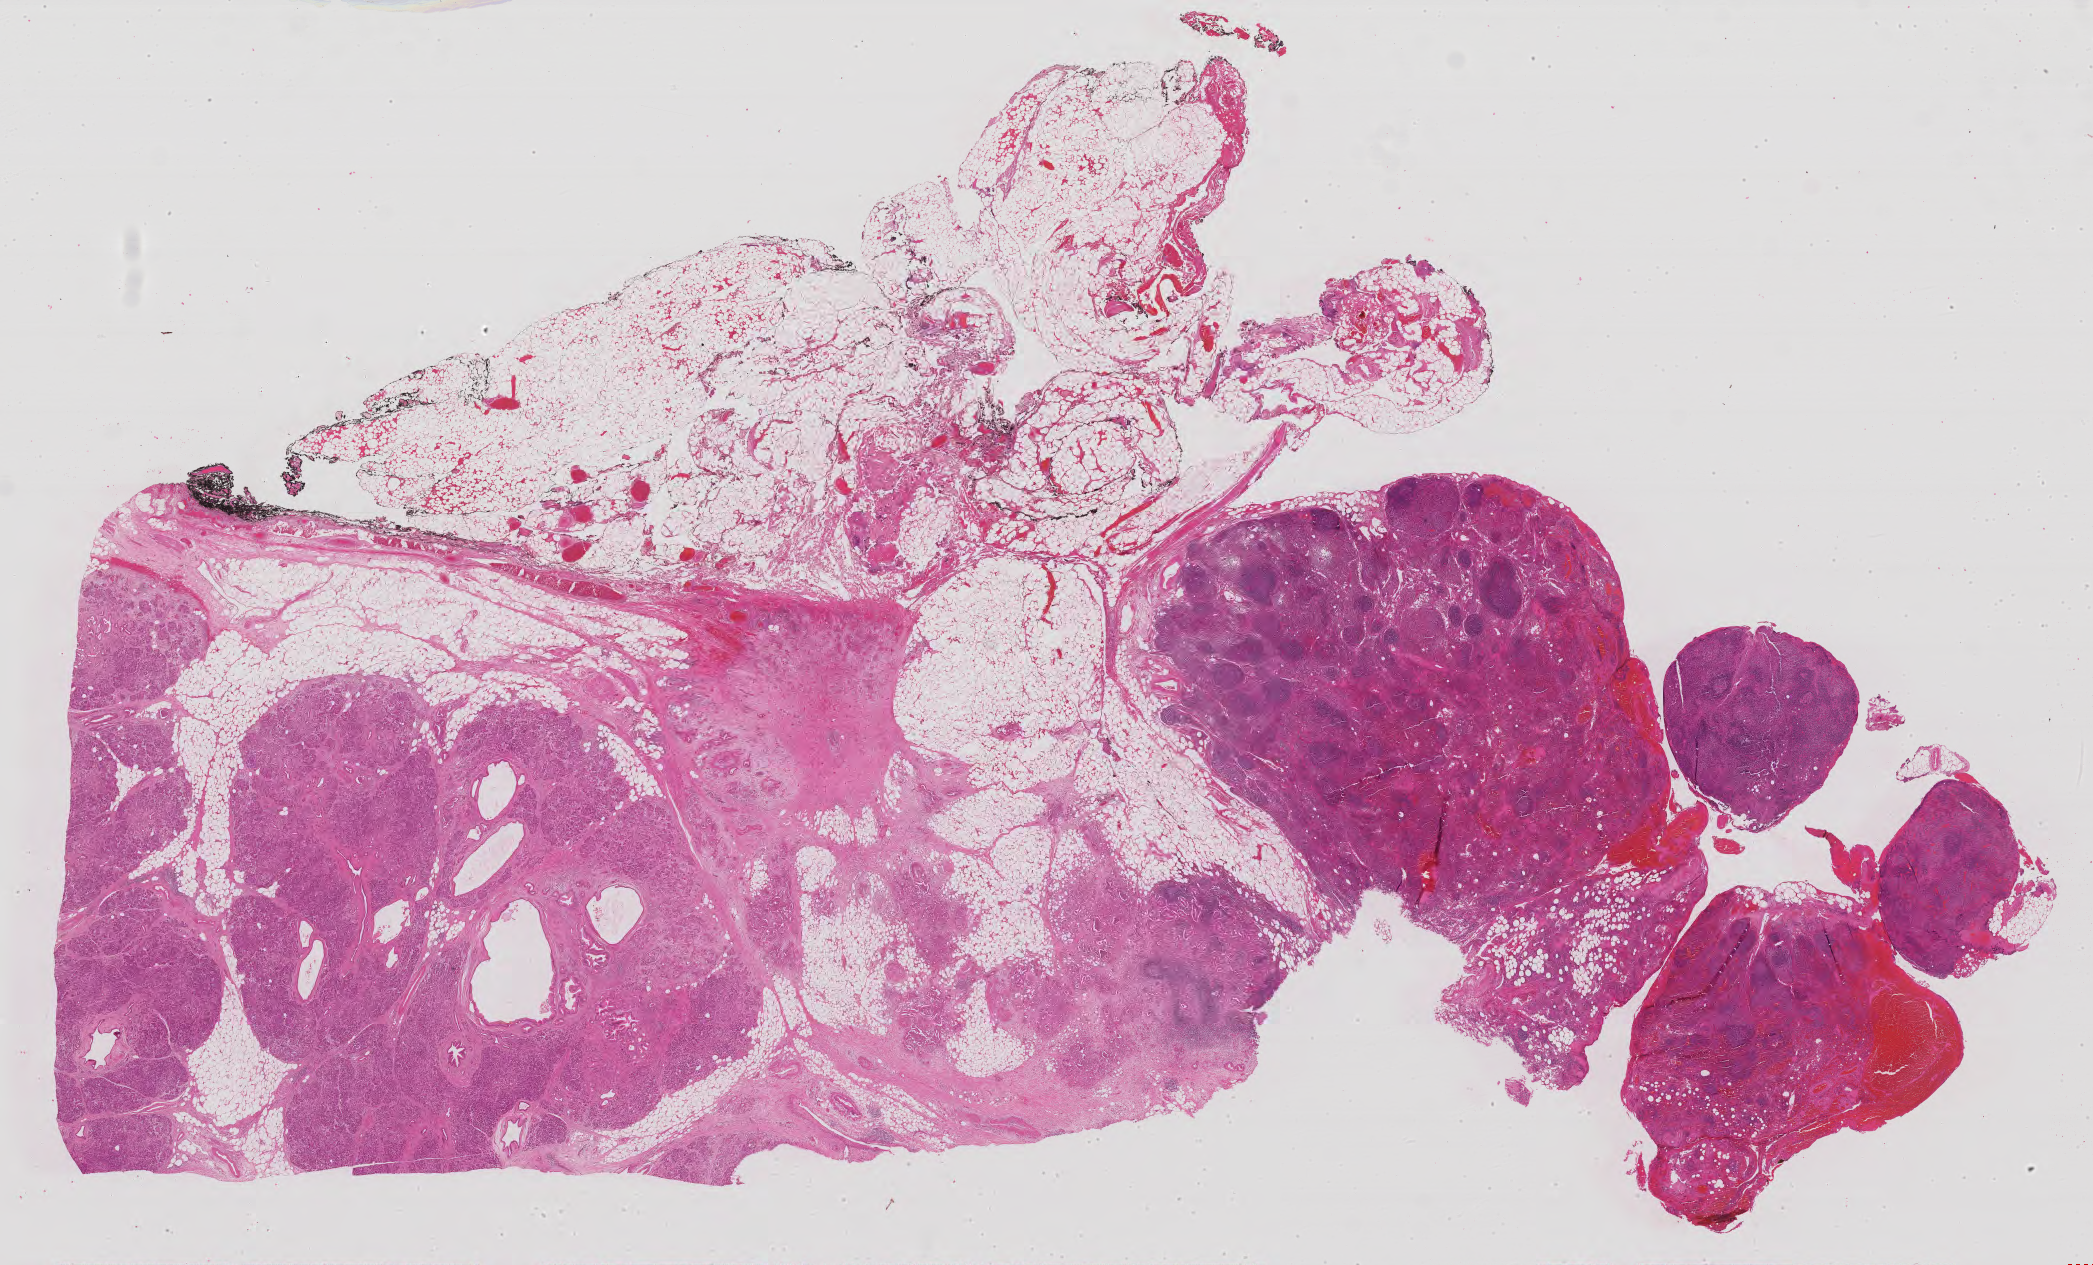
Whole-slide histology image, H&E — a low-resolution overview of the entire scanned area, about 33.5 x 20.2 mm; formalin-fixed paraffin-embedded (FFPE) diagnostic section; pancreas, primary tumour sample. Patient: male, age at initial diagnosis 67 years. Histologic grade: G3 (poorly differentiated).
TNM: T3 N1 MX. Lymph nodes positive (case pathology): 5 of 23 examined. AJCC pathologic stage: IIB (6th edition). Diagnosis: Infiltrating duct carcinoma, NOS (body of pancreas).